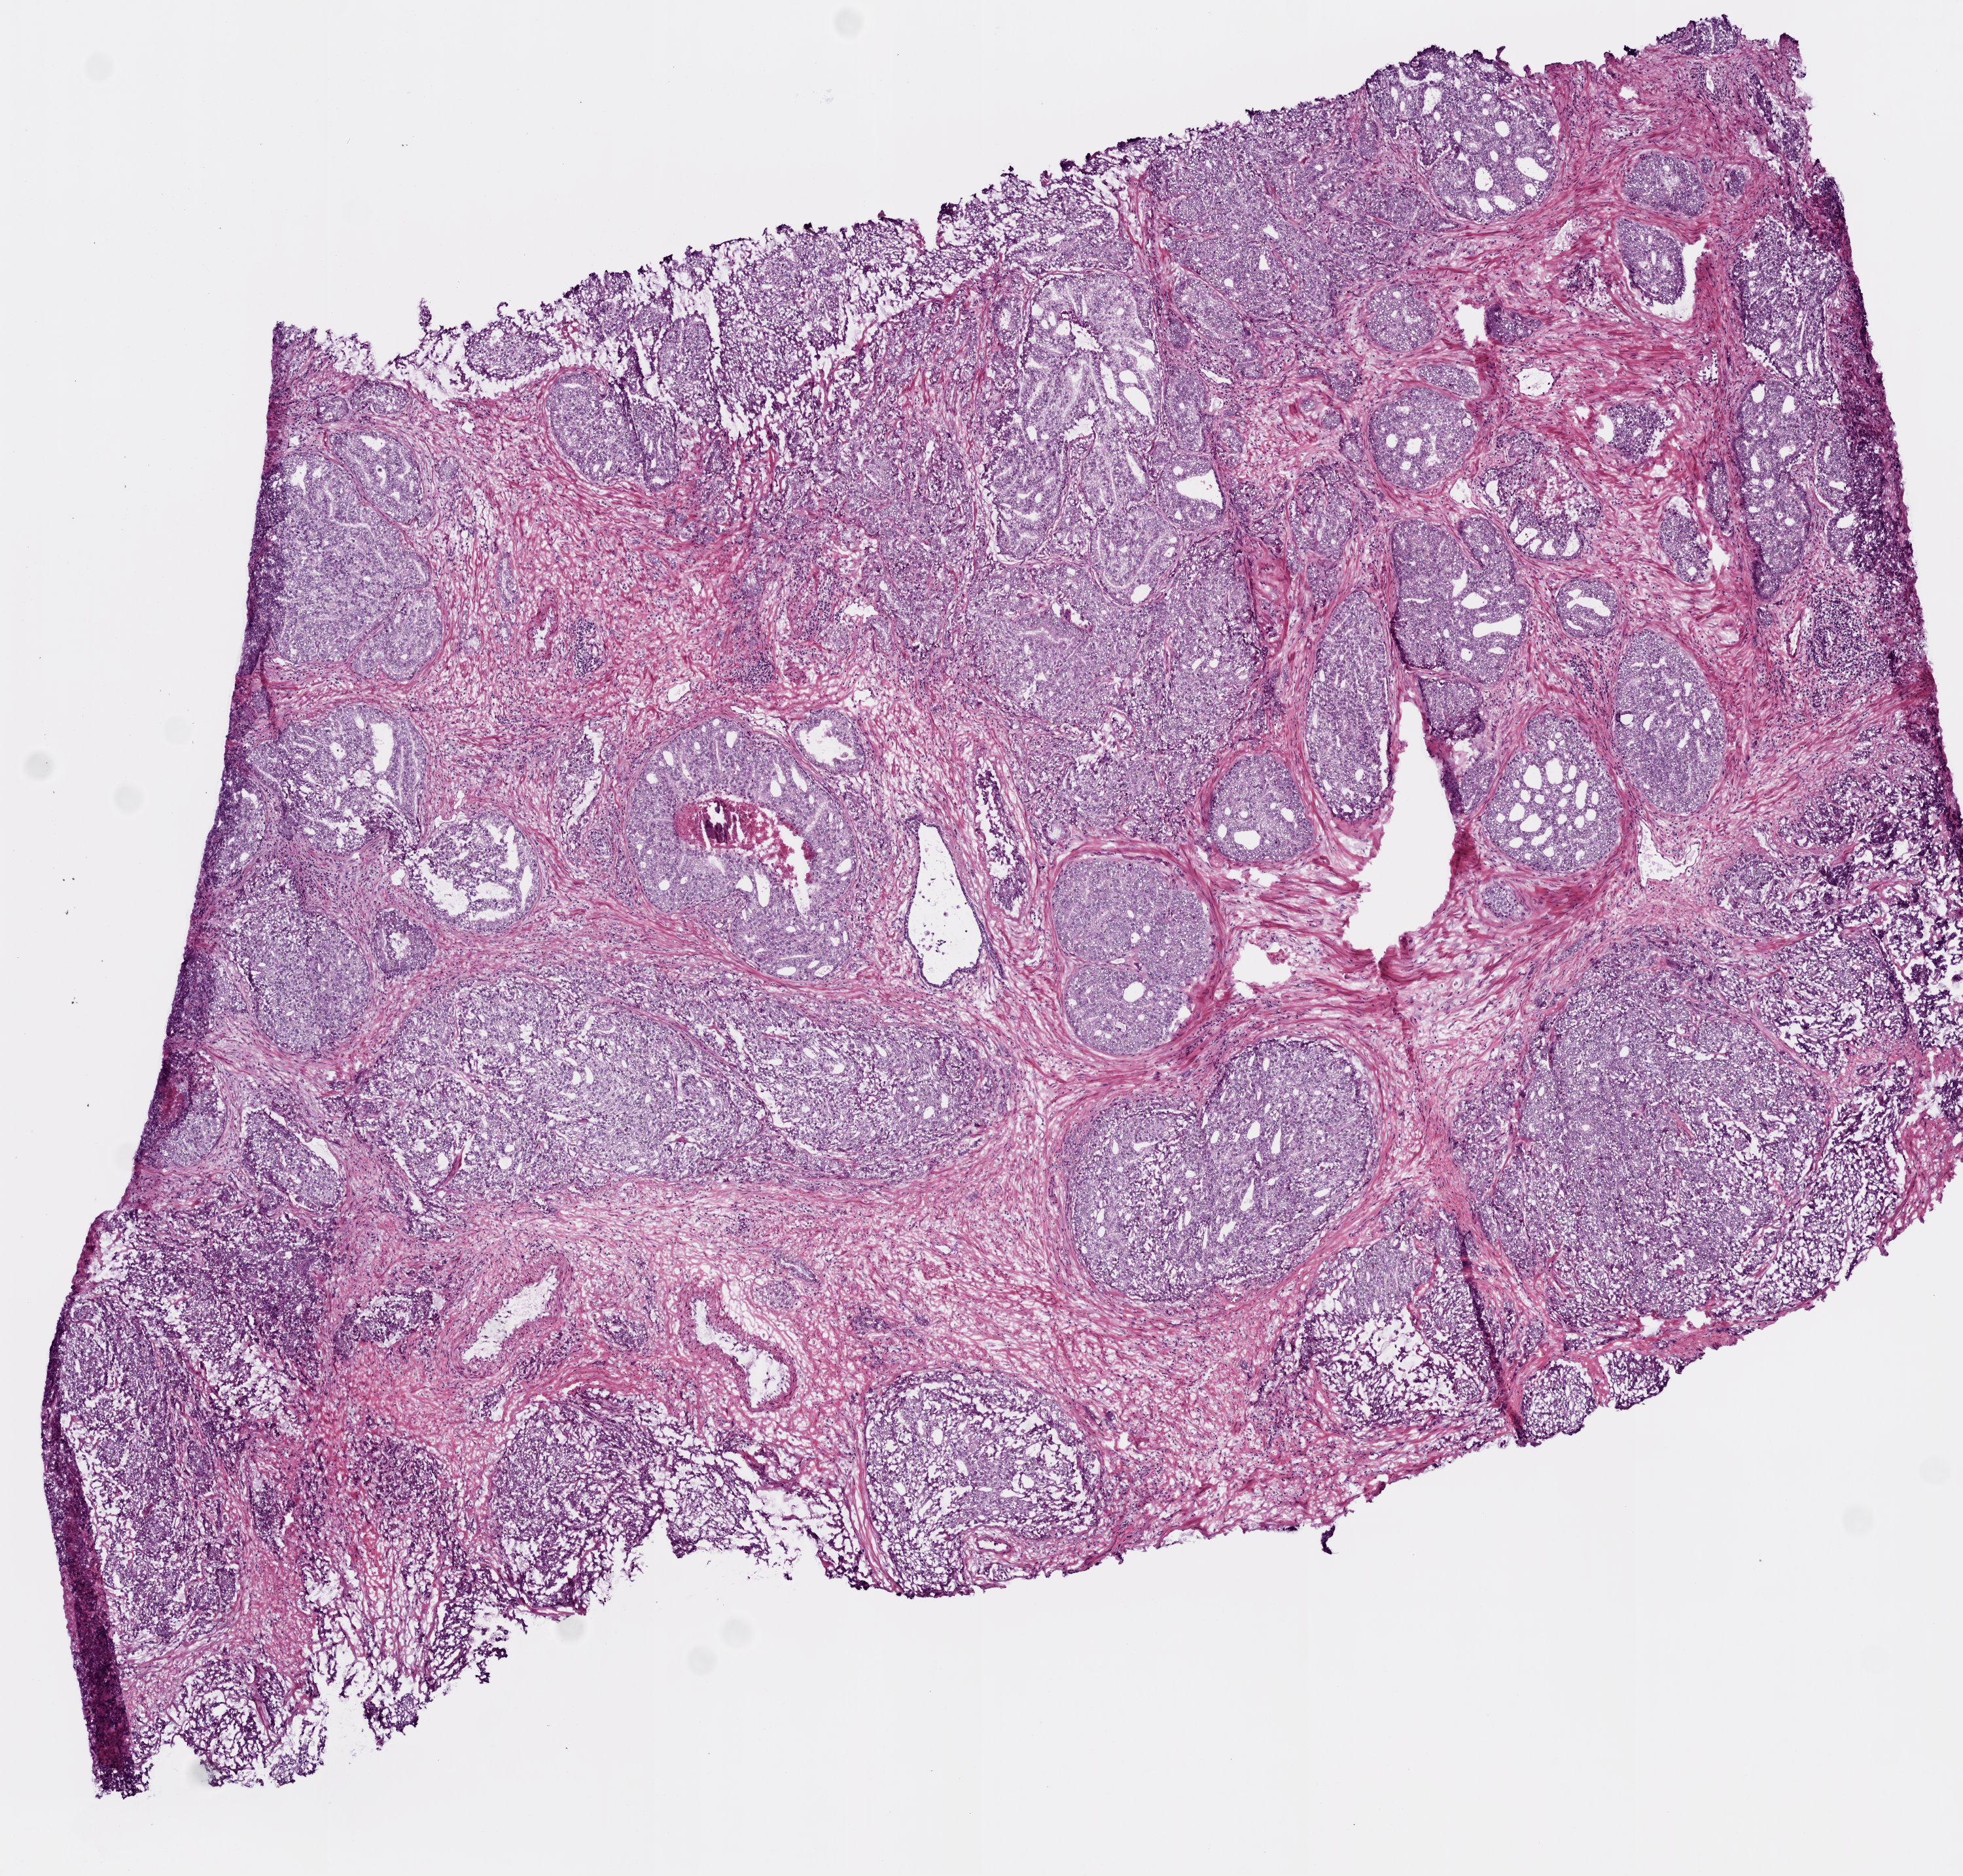
Hematoxylin and eosin (H&E) stained whole-slide image, a low-resolution overview of the entire scanned area, about 6.0 x 5.8 mm (slide scanned at 20x). Frozen section from the top of the tissue portion. Primary tumour sample from the prostate. Male, age 69 years at initial diagnosis. Gleason score: 7 (4+3). Composition of this section per pathologist review: tumour cells 75%, tumour nuclei 80%, normal cells 0%, stromal cells 20%, necrosis 5%. Inflammatory infiltration, as recorded: lymphocyte infiltration 3%, monocyte infiltration 3%, neutrophil infiltration 0%.
Lymph nodes positive (case pathology): 6 of 21 examined. Laterality: bilateral. Histologic diagnosis: Acinar cell carcinoma (prostate gland).